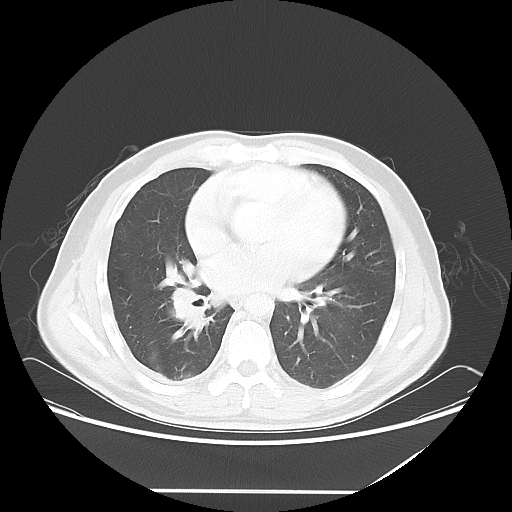
Chest CT, one axial slice; position 28 of 60 along the scan axis; reconstruction kernel LUNG; 120 kVp; lung window (W 1500 / L -600 HU); 5 mm slice thickness; 512 × 512 image matrix, field of view 419 × 419 mm. Male patient, age 48 years. Case-level facts recorded for this patient, not image findings: clinical TNM (as recorded): T3 N3 M1a.
Structures marked on this image (rectangle marked by the reading radiologist):
- lung tumour (recorded histology: squamous cell carcinoma): bounding box (x1, y1, x2, y2) in pixels: (166, 280, 211, 334)